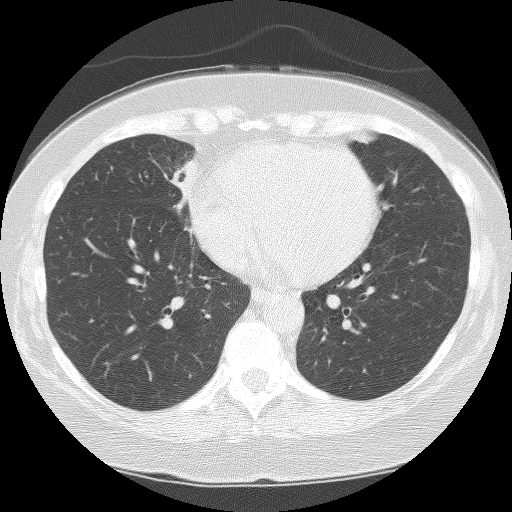
Low-dose screening chest CT, one axial slice; slice 71 of 159 in the series (ordered by position); 120 kVp; lung window (W 1500 / L -600 HU); 2.5 mm slice thickness; 512 × 512 image matrix, field of view 299 × 299 mm.
Structures marked on this image (outlined manually by an expert reader):
- lesion 1 (tumor, hilum of right lung): box from (x=172, y=159) to (x=196, y=202) px